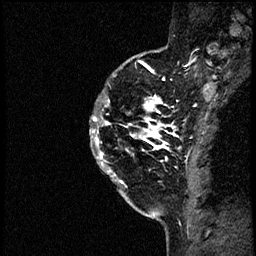
Breast MRI (dynamic contrast-enhanced), one sagittal slice. Position 46 of 60 along the scan axis. Dynamic contrast-enhanced study with each time point stored as its own series, time point 2 of 4 at this slice position (early post-contrast, ordered by acquisition time). 1.5 T. TE 4.2 ms, TR 17.6 ms. 2 mm slice thickness. 256 × 256 image matrix. Female patient, age 40 years. Case-level facts recorded for this patient, not image findings: setting: breast cancer imaged before/during neoadjuvant chemotherapy; receptor status: HER2-positive.
Outlined on this slice (semi-automatically segmented with operator editing):
- analysis volume of interest (the breast-tissue region the enhancement analysis was run in; not a lesion): box from (x=91, y=56) to (x=197, y=205) px
- tumour enhancement mask (voxels above the 100 % enhancement threshold inside the analysis volume of interest): (x=92, y=61)–(x=197, y=197)